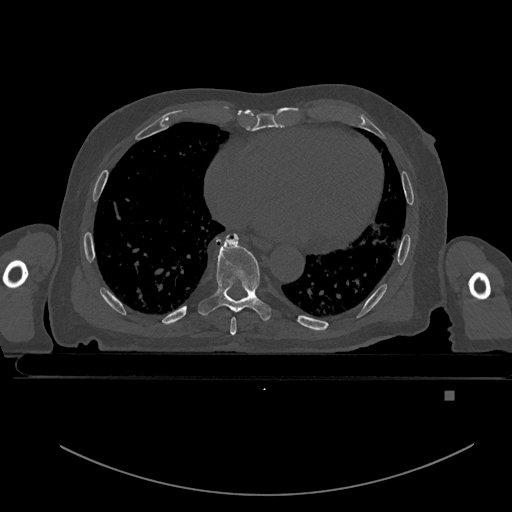
CT including the spine, one axial slice. Position 206 of 969 along the scan axis. Bone window (W 1800 / L 400 HU). 0.5 mm slice thickness. 512 × 512 image matrix, field of view 456 × 456 mm. Patient: male, 82 years. Case-level facts recorded for this patient, not image findings: primary cancer: prostate; vertebrae with lytic lesions (as recorded): T11, T9, T8, T2.
Structures marked on this image (semi-automatic segmentation, software-assisted and operator-edited):
- T7 vertebra: bounding box [x1, y1, x2, y2] px = [230, 317, 236, 335]
- T8 vertebra: [198, 234, 272, 321]